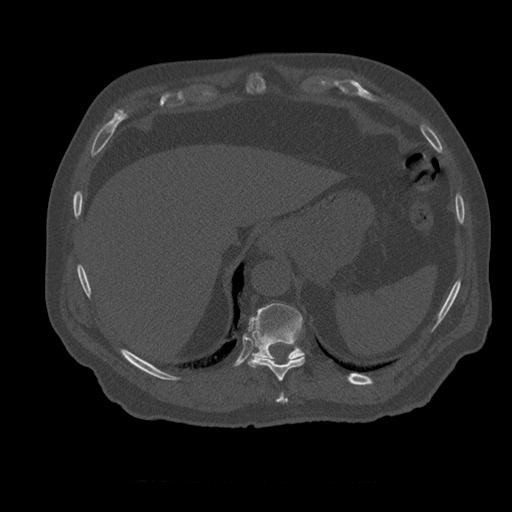
CT including the spine, one axial slice; position 294 of 399 along the scan axis; 120 kVp; bone window (W 1800 / L 400 HU); 512 × 512 image matrix, field of view 407 × 407 mm. Patient age 73 years. From the clinical record (not read from this slice): primary cancer: prostate; vertebrae with lytic lesions (as recorded): L2.
Outlined on this slice (semi-automatically segmented with operator editing):
- T10 vertebra: bounding box <248,342,305,382> (left, top, right, bottom; pixels)
- T11 vertebra: <248,303,304,361>
- T9 vertebra: <277,393,289,403>